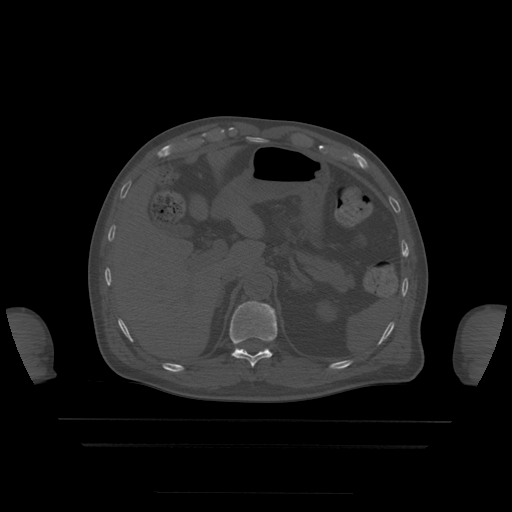
CT including the spine, one axial slice; position 216 of 522 along the scan axis; bone window (W 1800 / L 400 HU); 1.25 mm slice thickness; 512 × 512 image matrix, field of view 436 × 436 mm. Patient age 68 years. Case-level facts recorded for this patient, not image findings: primary cancer: urothelial.
Annotated regions visible in this slice (semi-automatic segmentation, software-assisted and operator-edited):
- T11 vertebra: bounding box (x1, y1, x2, y2) in pixels: (230, 301, 278, 368)